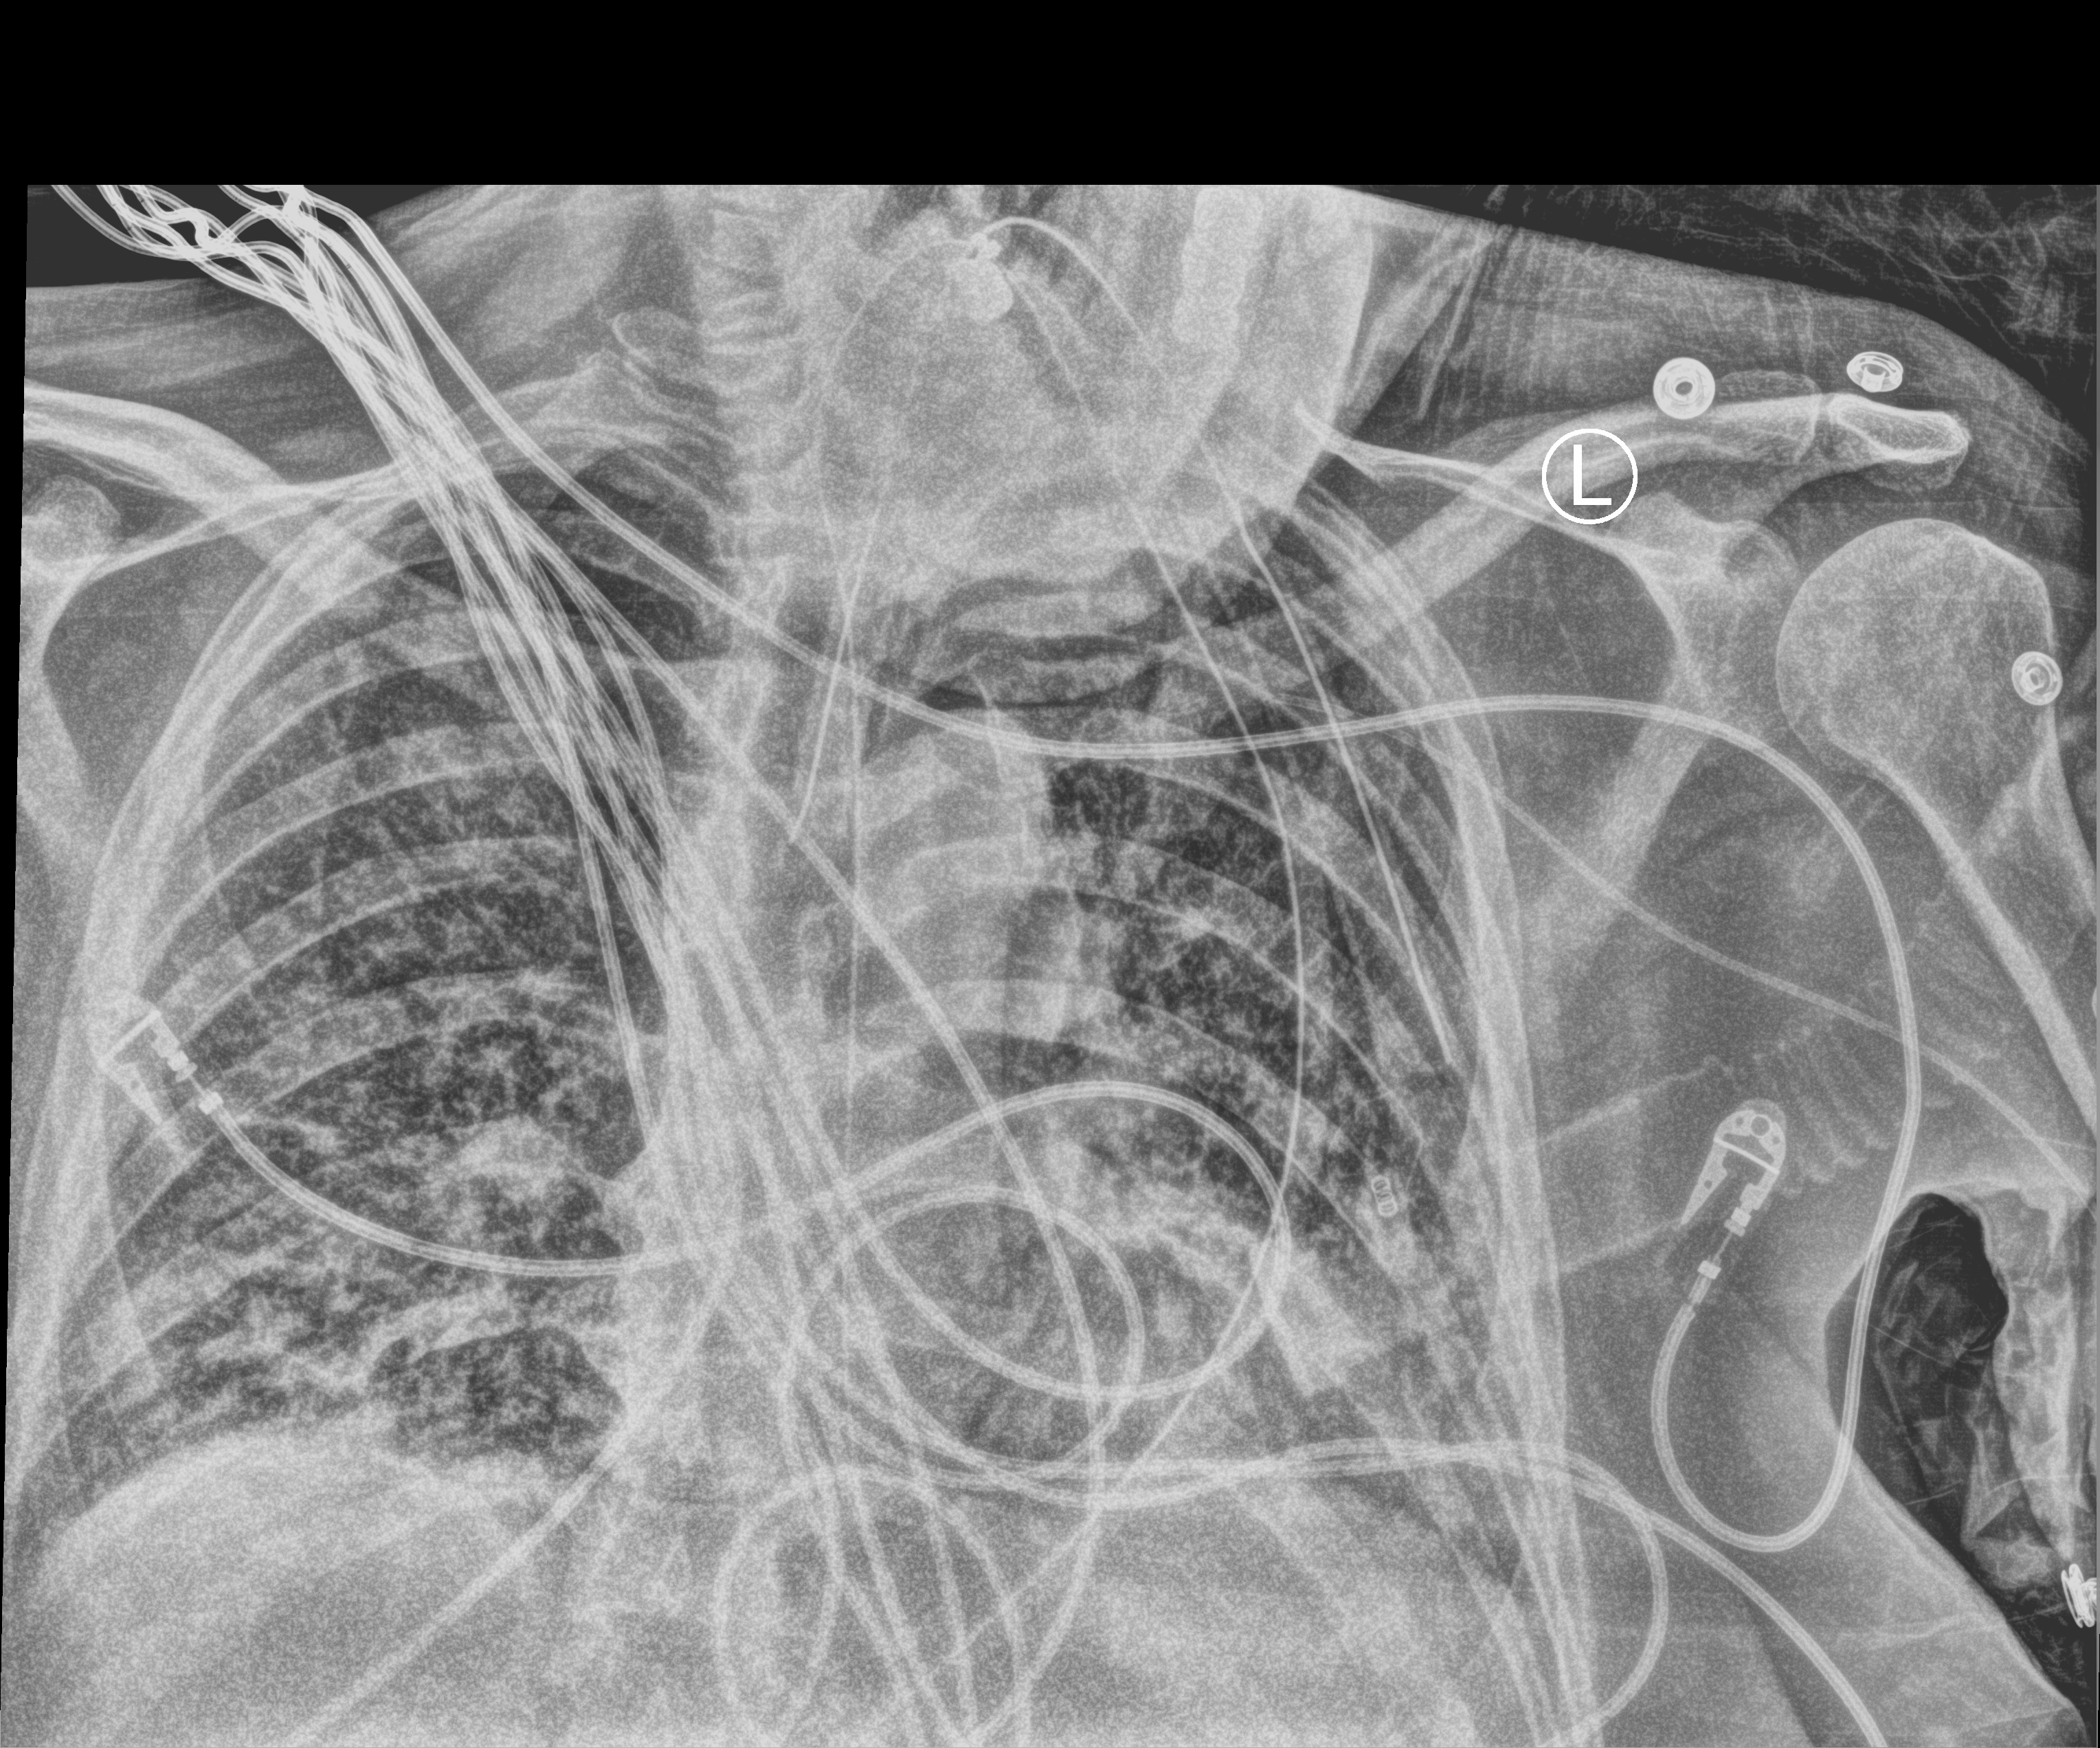
Bedside chest radiograph (computed radiography). Patient hospitalised with COVID-19; male, aged 60–74 years.
From the hospital-stay record, not from the radiograph (when in the stay this image was taken is not recorded):
- length of hospital stay: 40 days
- mechanically ventilated during this hospital stay: yes
- hypertension (admission record): yes